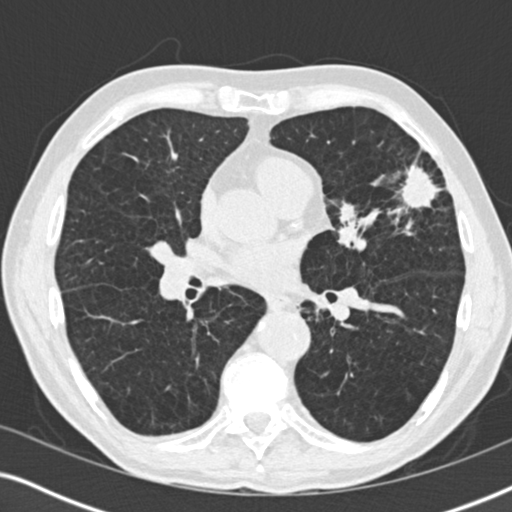
Low-dose screening chest CT, one axial slice; position 97 of 196 along the scan axis; 120 kVp; lung window (W 1500 / L -600 HU); 512 × 512 image matrix, field of view 330 × 330 mm.
Annotated regions visible in this slice (outlined manually by an expert reader):
- lesion 1 (tumor, upper lobe of left lung): bounding box (x1, y1, x2, y2) in pixels: (400, 164, 439, 209)
- lesion 2 (tumor, upper lobe of left lung): (338, 203, 356, 224)